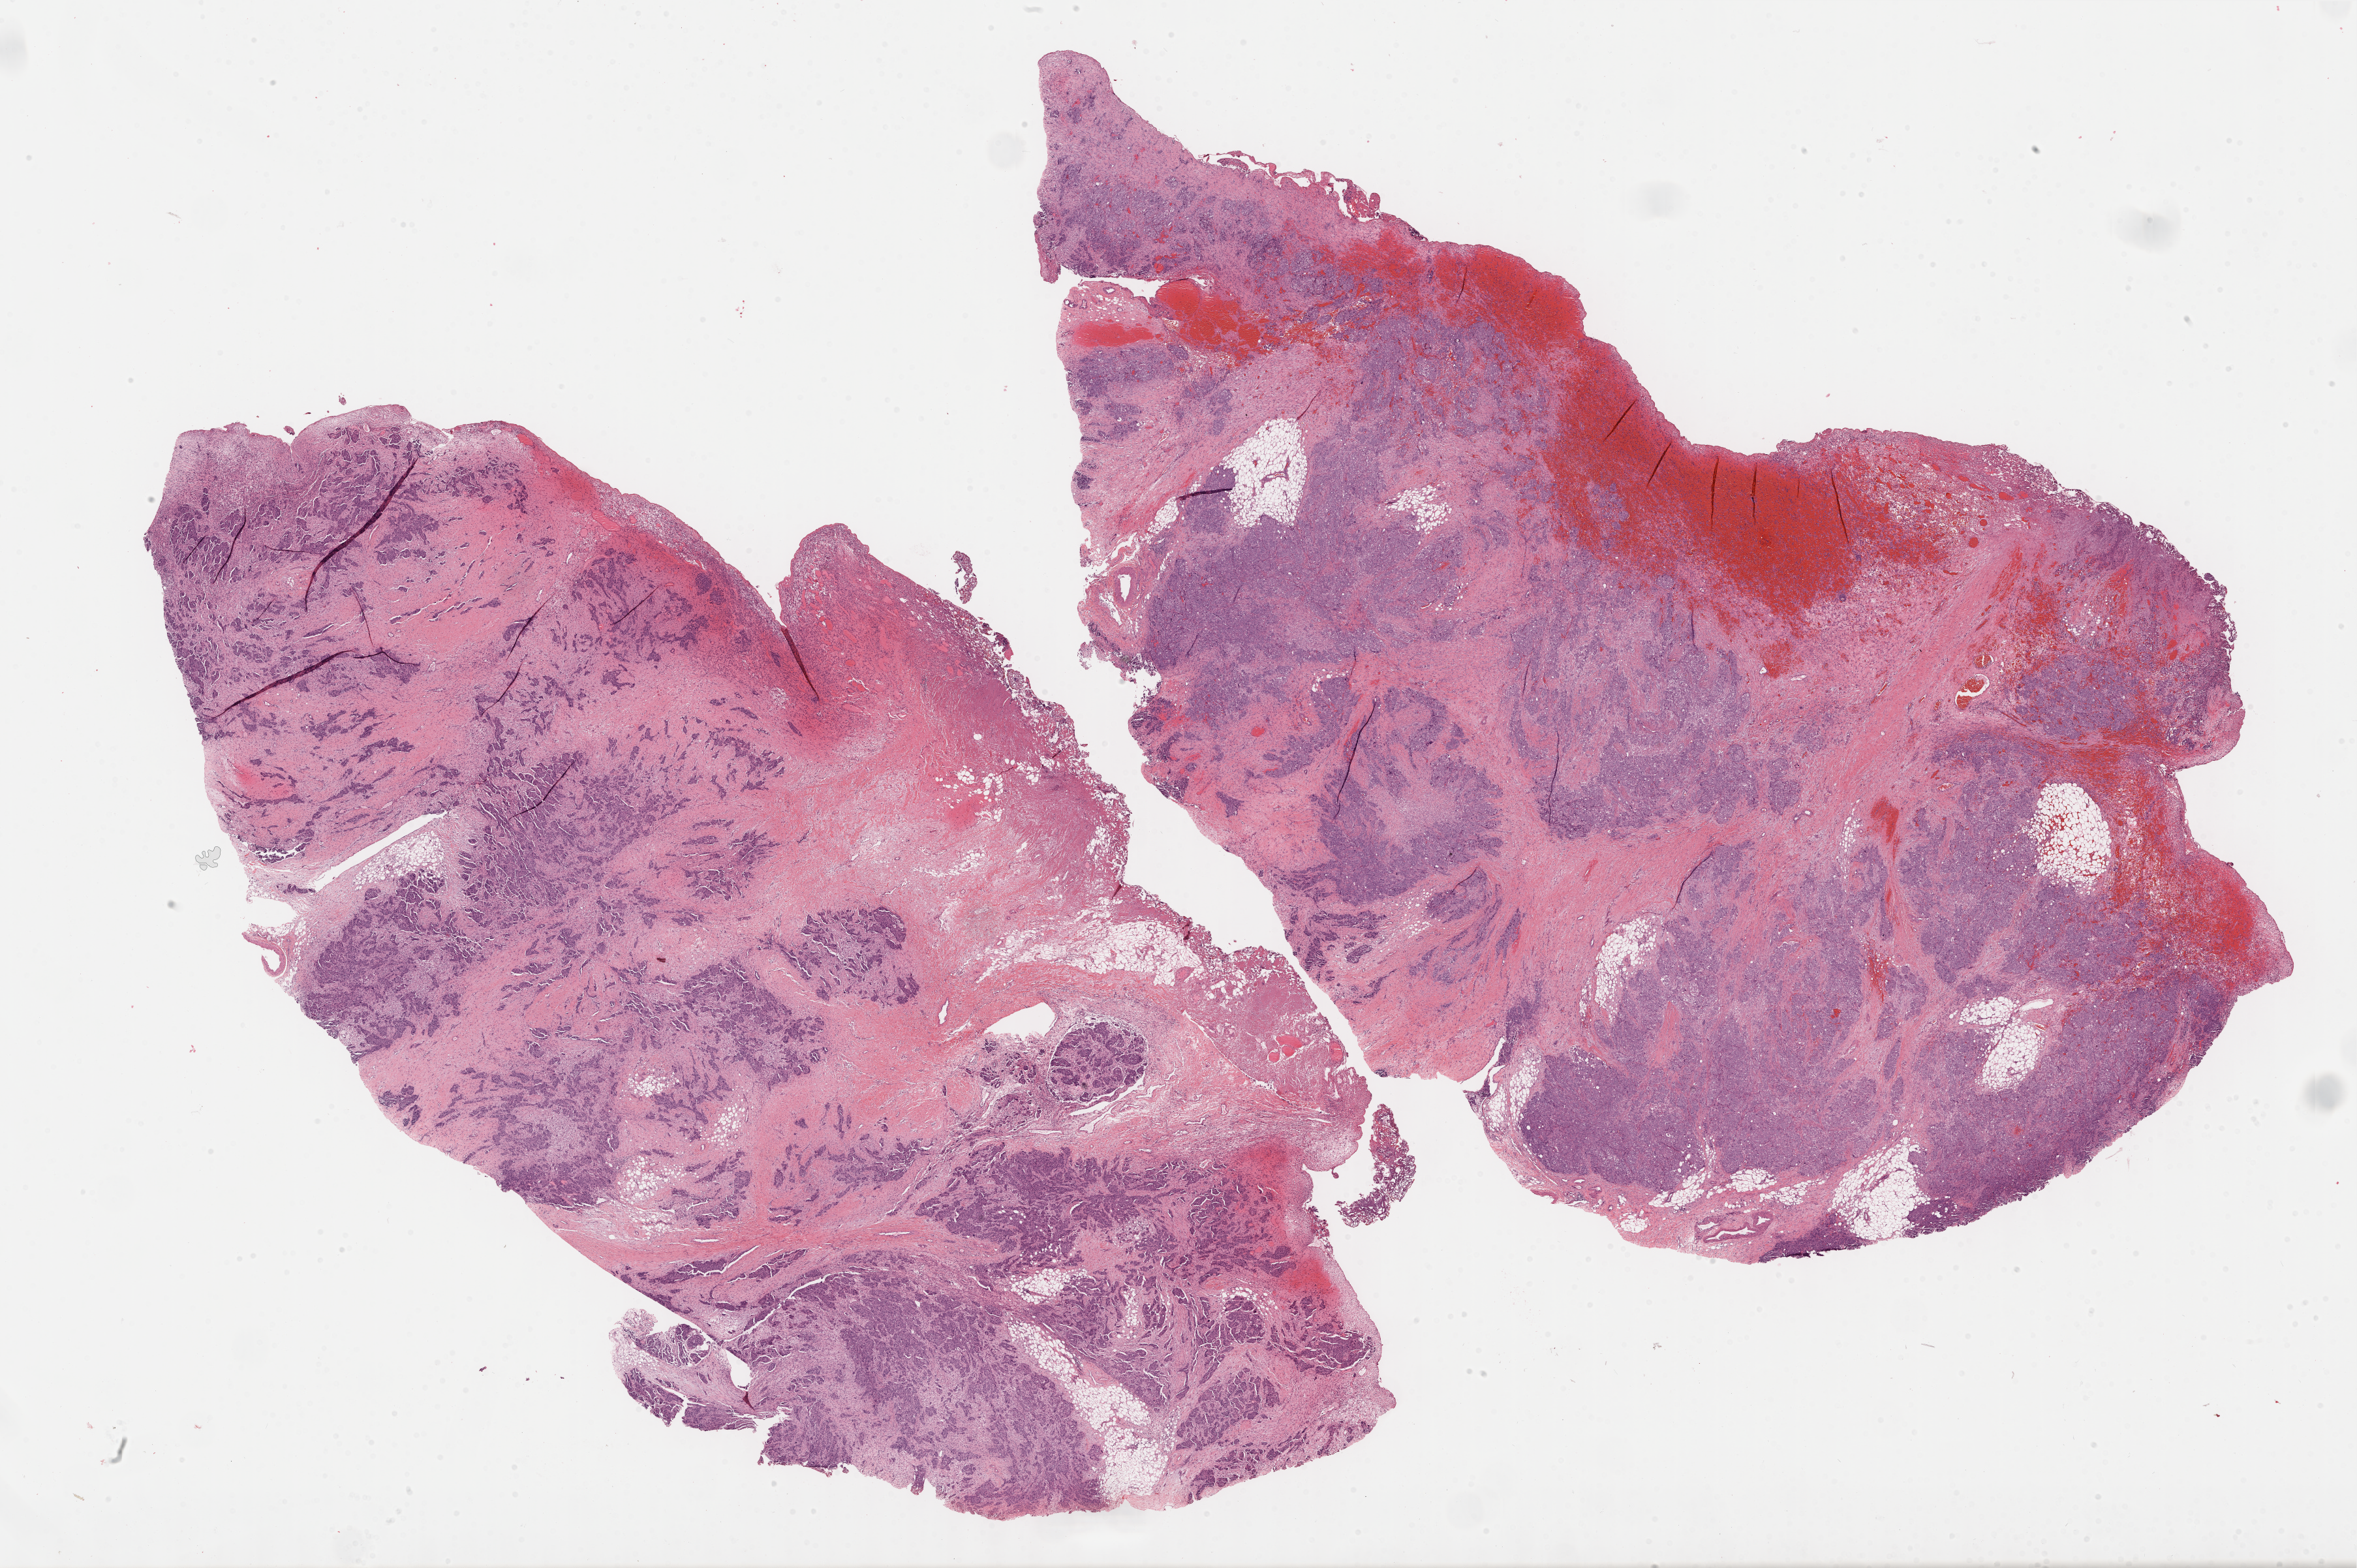
Whole-slide histology image, H&E-stained, low-resolution overview of the scanned area, about 29.2 x 19.4 mm (acquisition: 40x scan); FFPE section; ovary, primary tumour sample. Female patient; age at initial diagnosis 60 years. Histologic grade: G3 (poorly differentiated).
• FIGO stage: IIIC
• diagnosis: Serous cystadenocarcinoma, NOS